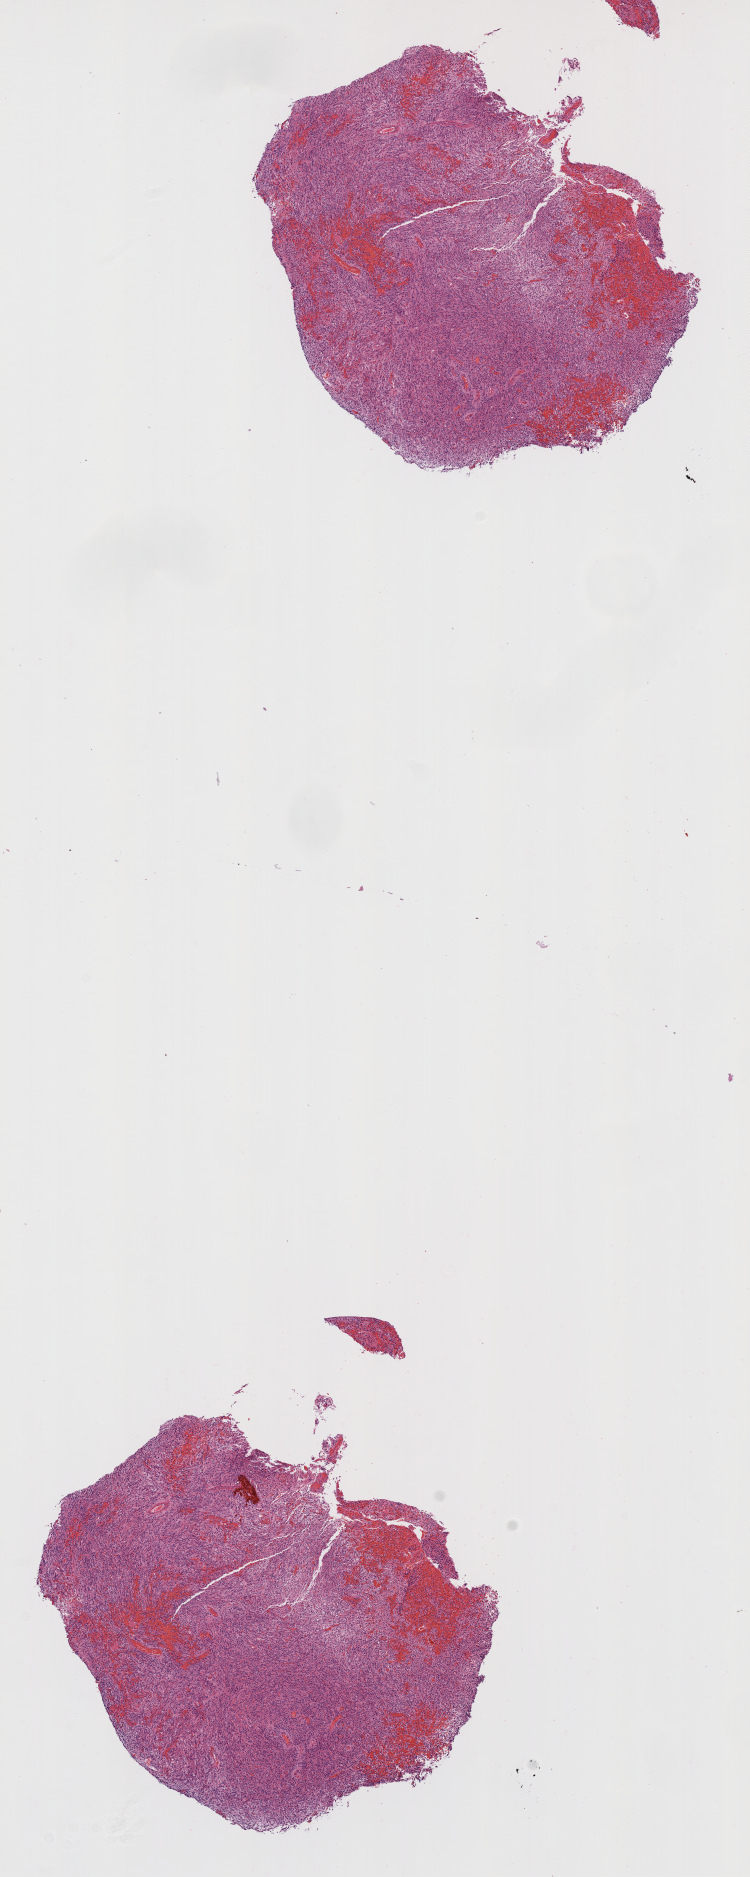
Digitized Hematoxylin and eosin (H&E) stained tissue section (whole slide), a low-resolution overview of the entire scanned area, about 6.0 x 15.1 mm (acquisition: 20x scan). FFPE section. Brain, primary tumour sample. Female, age 53 years at initial diagnosis.
Histologic diagnosis: Glioblastoma.